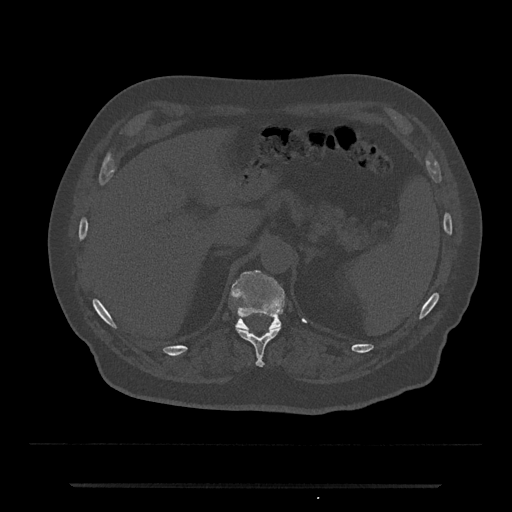
CT including the spine, one axial slice; slice 626 of 797 in the series (ordered by position); reconstruction kernel Br40s/3; bone window (W 1800 / L 400 HU); 0.5 mm slice thickness; 512 × 512 image matrix, field of view 434 × 434 mm. Patient: male, 80 years. From the clinical record (not read from this slice): primary cancer: prostate.
Annotated regions visible in this slice (semi-automatic segmentation, software-assisted and operator-edited):
- T11 vertebra: bounding box (x1, y1, x2, y2) in pixels: (237, 328, 281, 367)
- T12 vertebra: (231, 269, 286, 331)